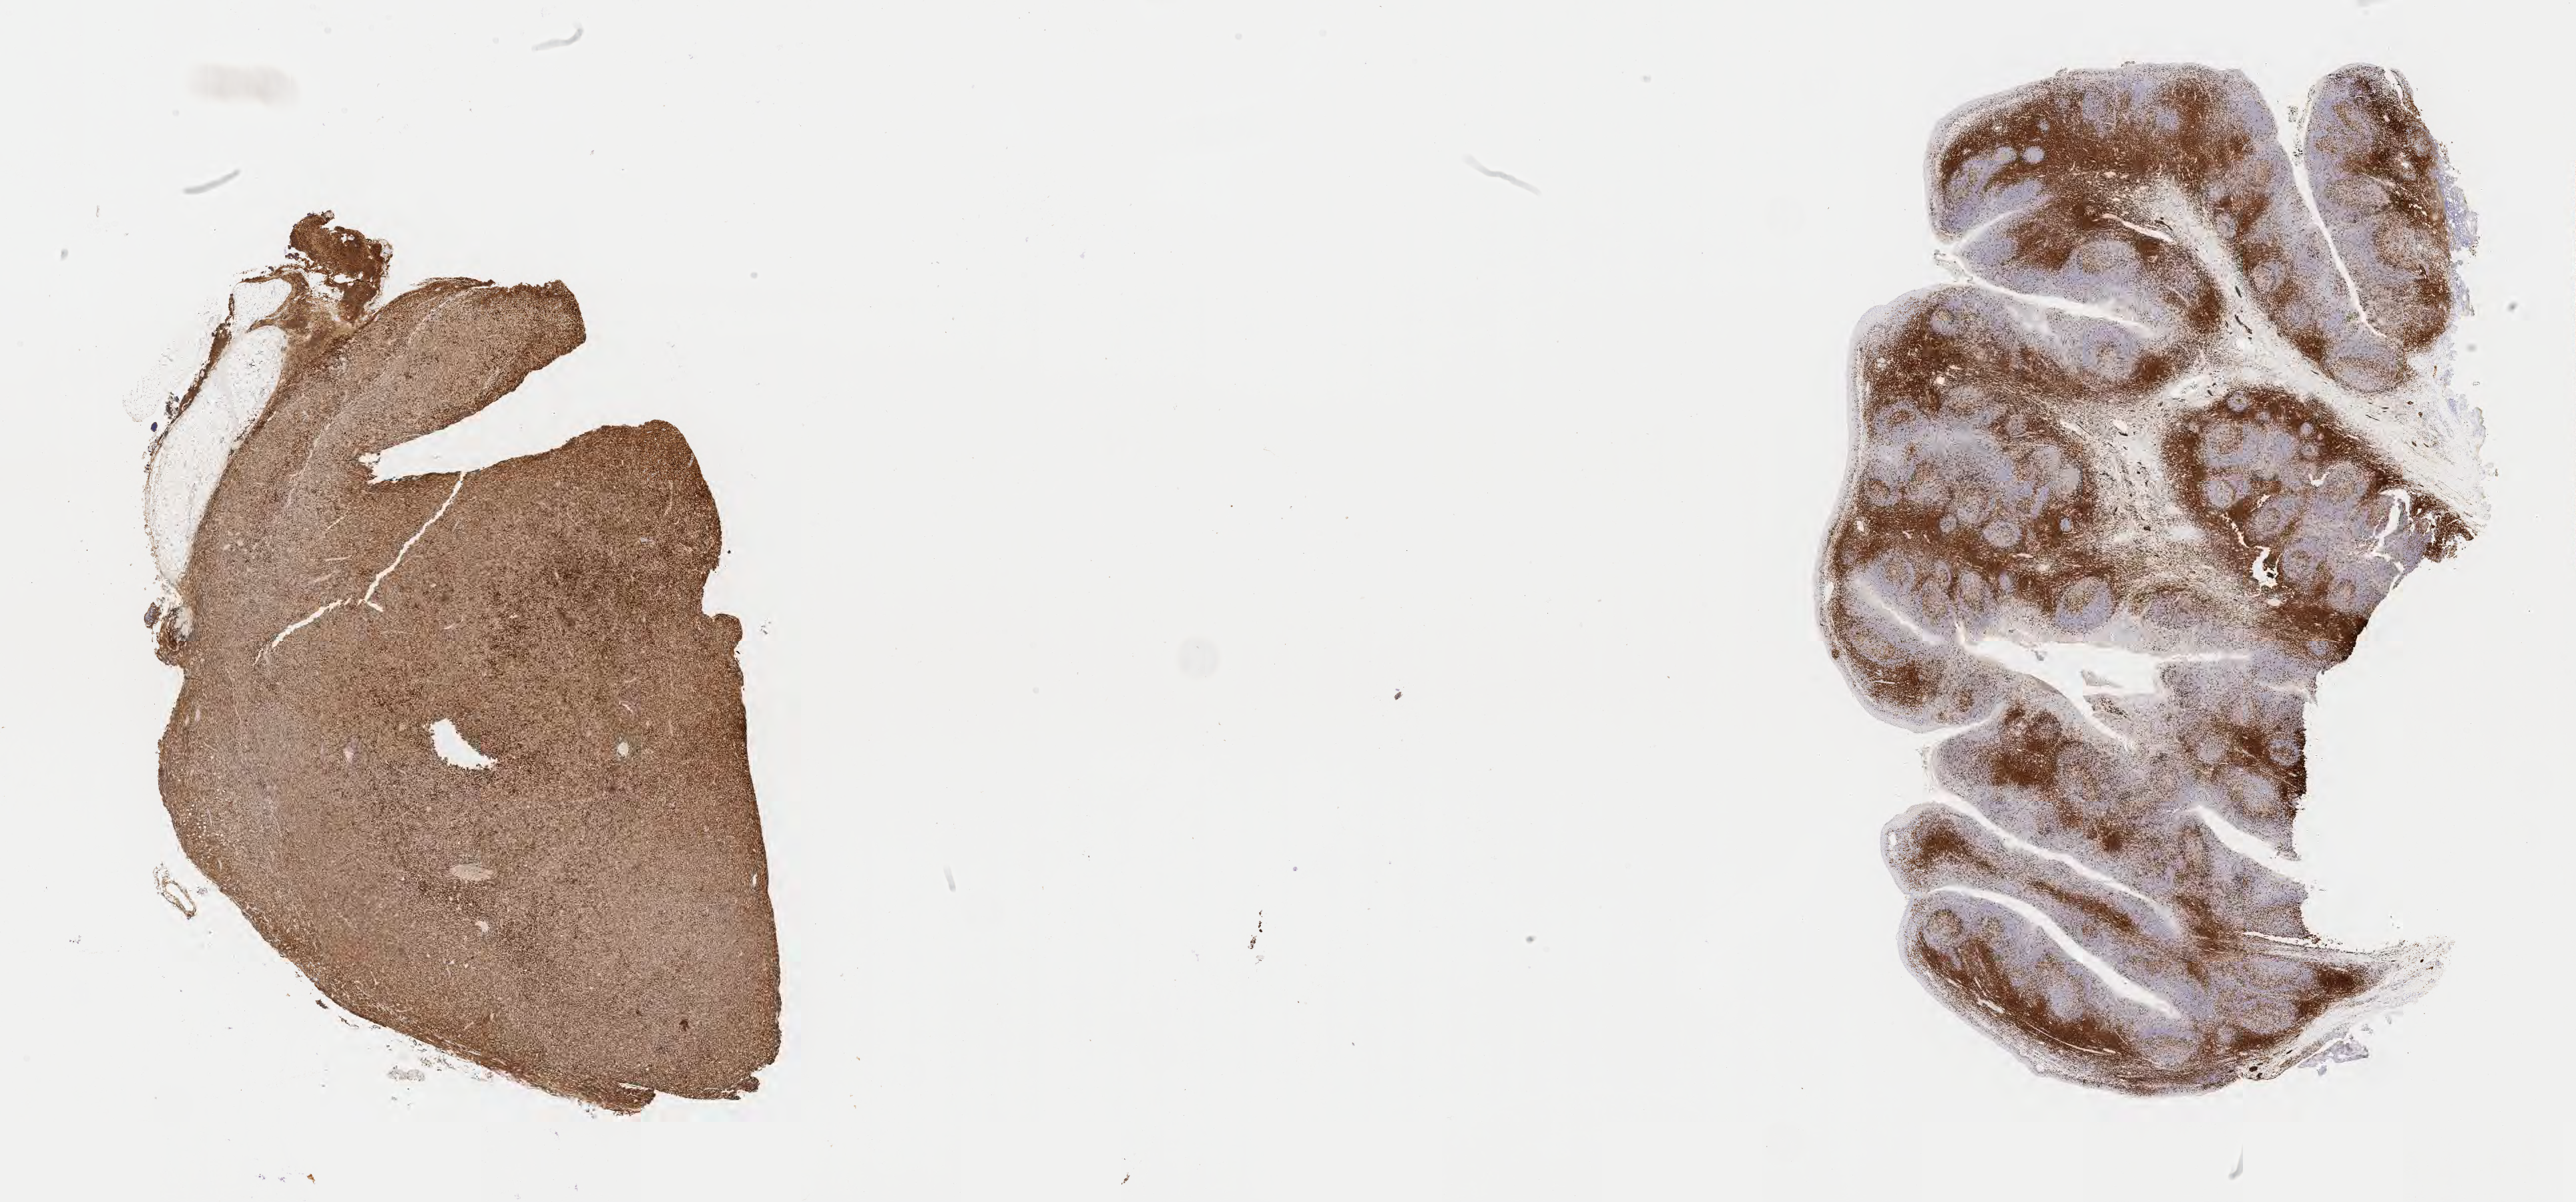
Whole-slide image, immunohistochemical stain for CD3, whole scanned area (about 31.2 x 14.6 mm) shown as a low-resolution overview; tumor tissue; site: lymph node. Patient male; aged 26.
* histologic diagnosis: Diffuse large B-cell lymphoma, NOS